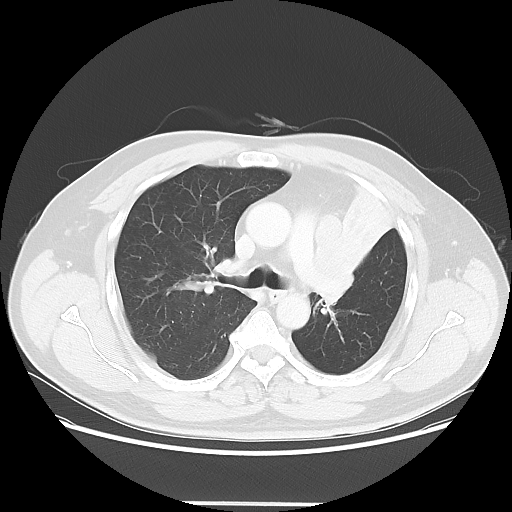
Chest CT, one axial slice. Slice 40 of 62 in the series (ordered by position). 120 kVp. Lung window (W 1500 / L -600 HU). 512 × 512 image matrix, field of view 403 × 403 mm. Patient: male, 49 years. From the clinical record (not read from this slice): clinical TNM (as recorded): T3 N3 M1c.
Outlined on this slice (bounding box drawn by a radiologist):
- lung tumour (recorded histology: squamous cell carcinoma): bounding box [x1, y1, x2, y2] px = [304, 212, 356, 303]